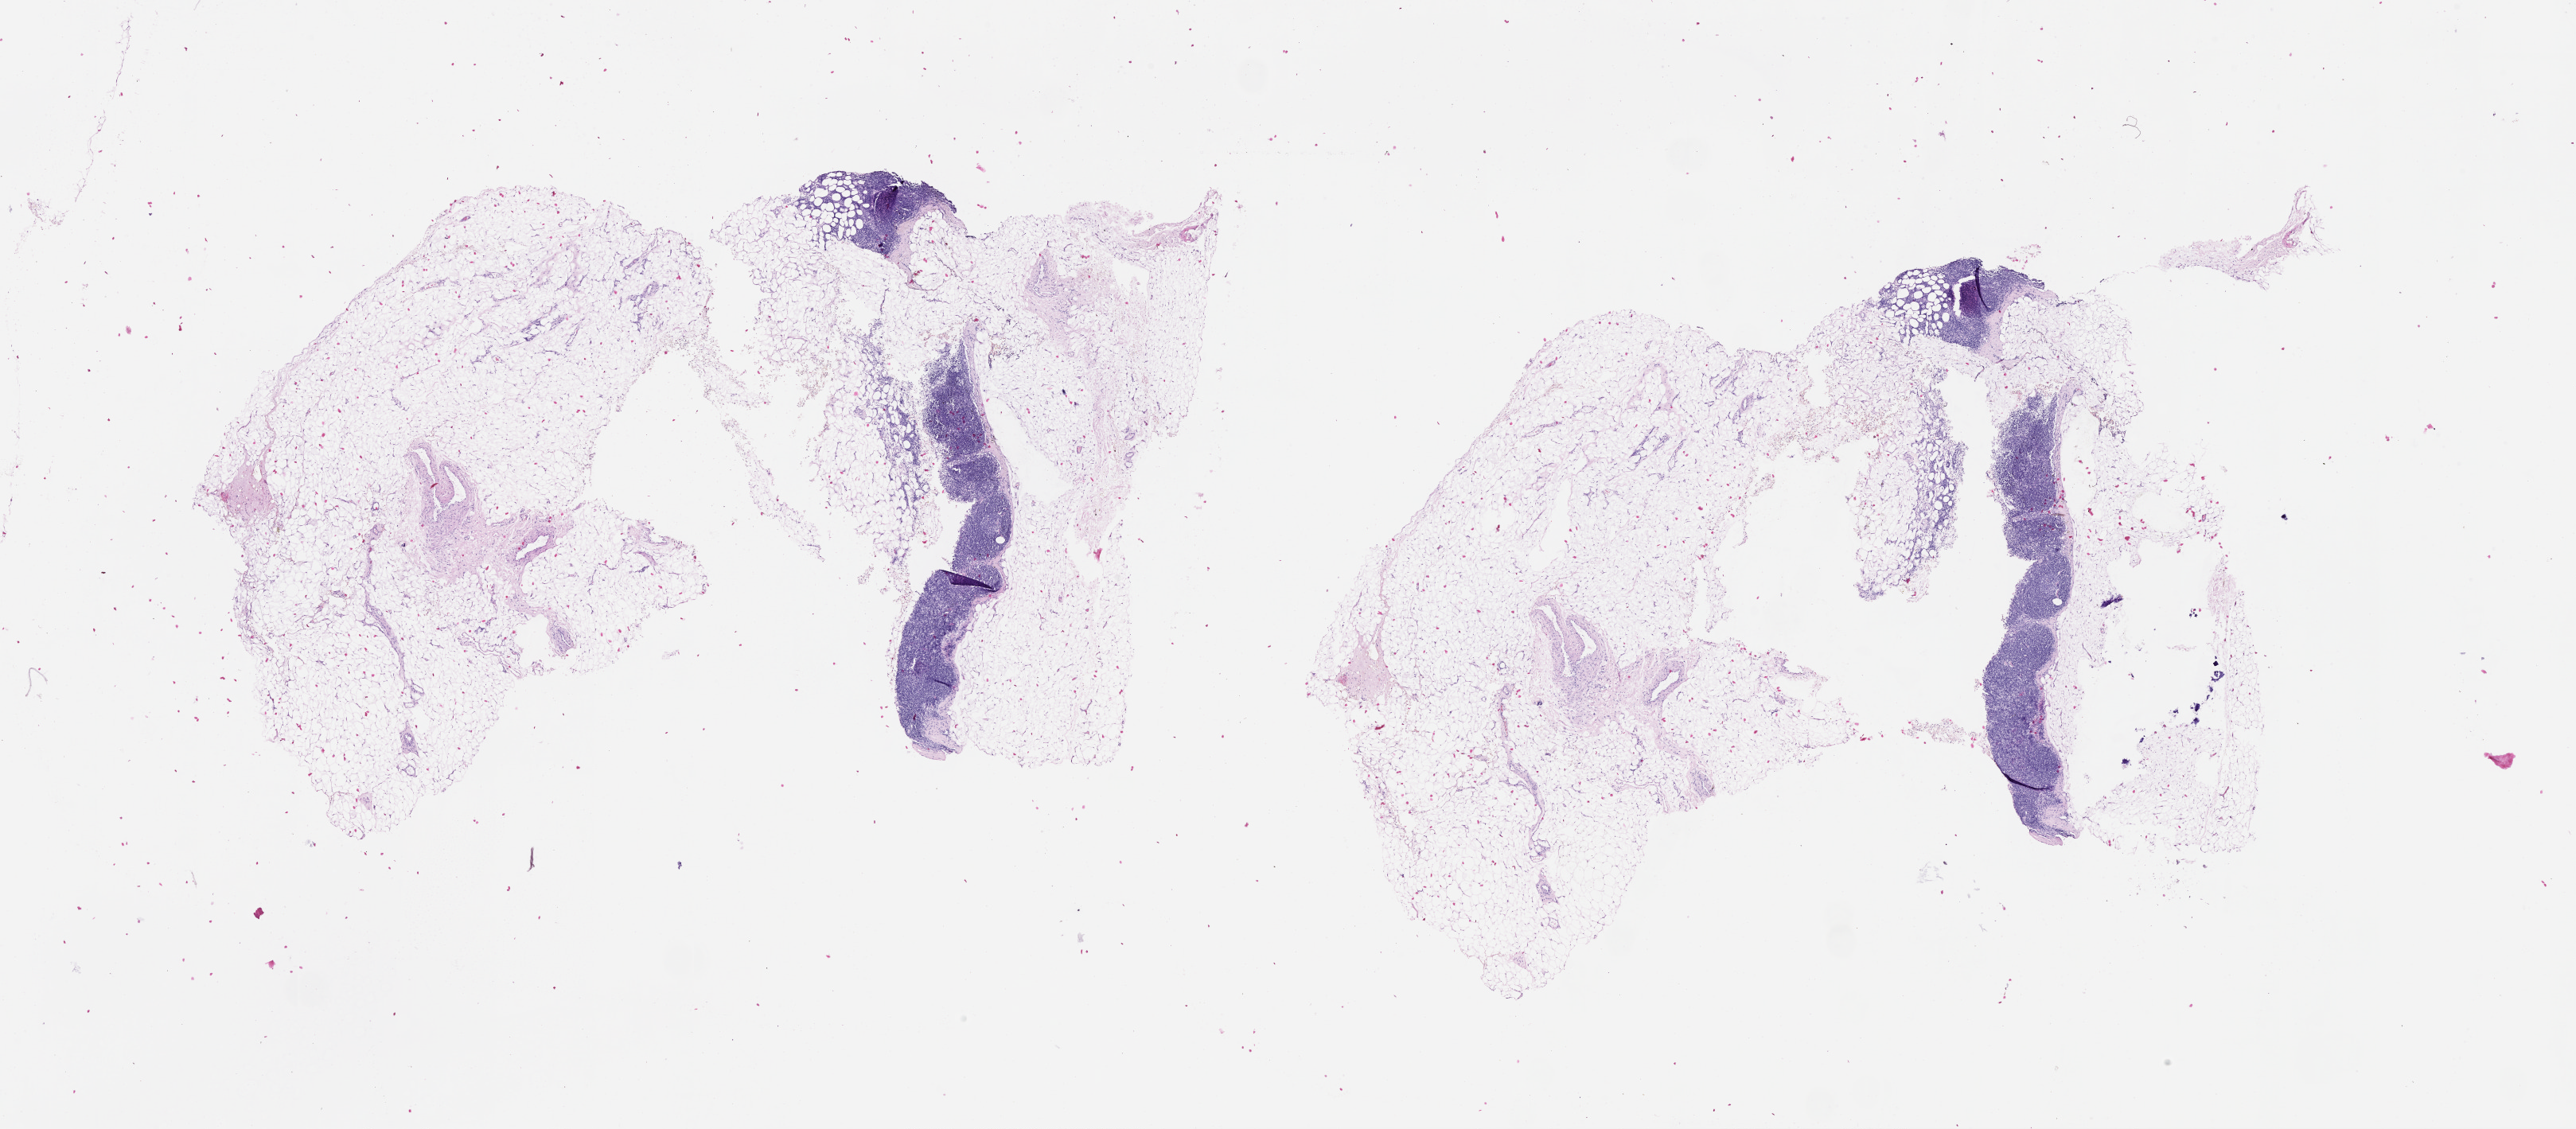
Whole-slide histology image, H&E-stained, a low-resolution overview of the entire scanned area, about 26.1 x 11.4 mm; normal (non-tumour) tissue sample, sampled site: lymph node. Patient: male, age 72 years.
* this section: normal (non-tumour) tissue from the same patient
* patient diagnosis: Malignant melanoma, NOS